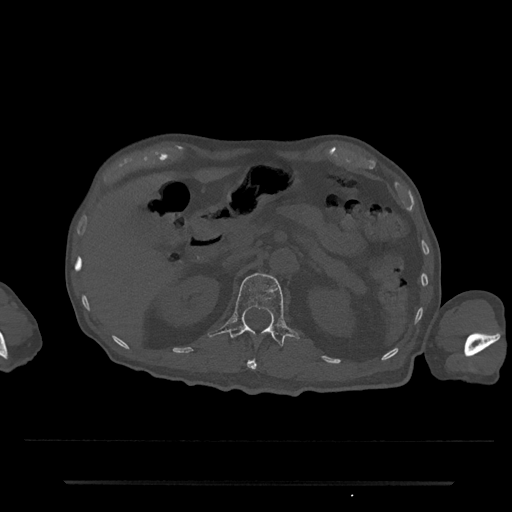
CT including the spine, one axial slice; reconstruction kernel Br40s/3; 120 kVp; bone window (W 1800 / L 400 HU); 512 × 512 image matrix, field of view 427 × 427 mm. Male patient, age 74 years. Case-level facts recorded for this patient, not image findings: primary cancer: prostate.
Structures marked on this image (semi-automatically segmented with operator editing):
- L1 vertebra: bounding box (x1, y1, x2, y2) in pixels: (208, 273, 299, 347)
- T12 vertebra: (247, 359, 257, 370)